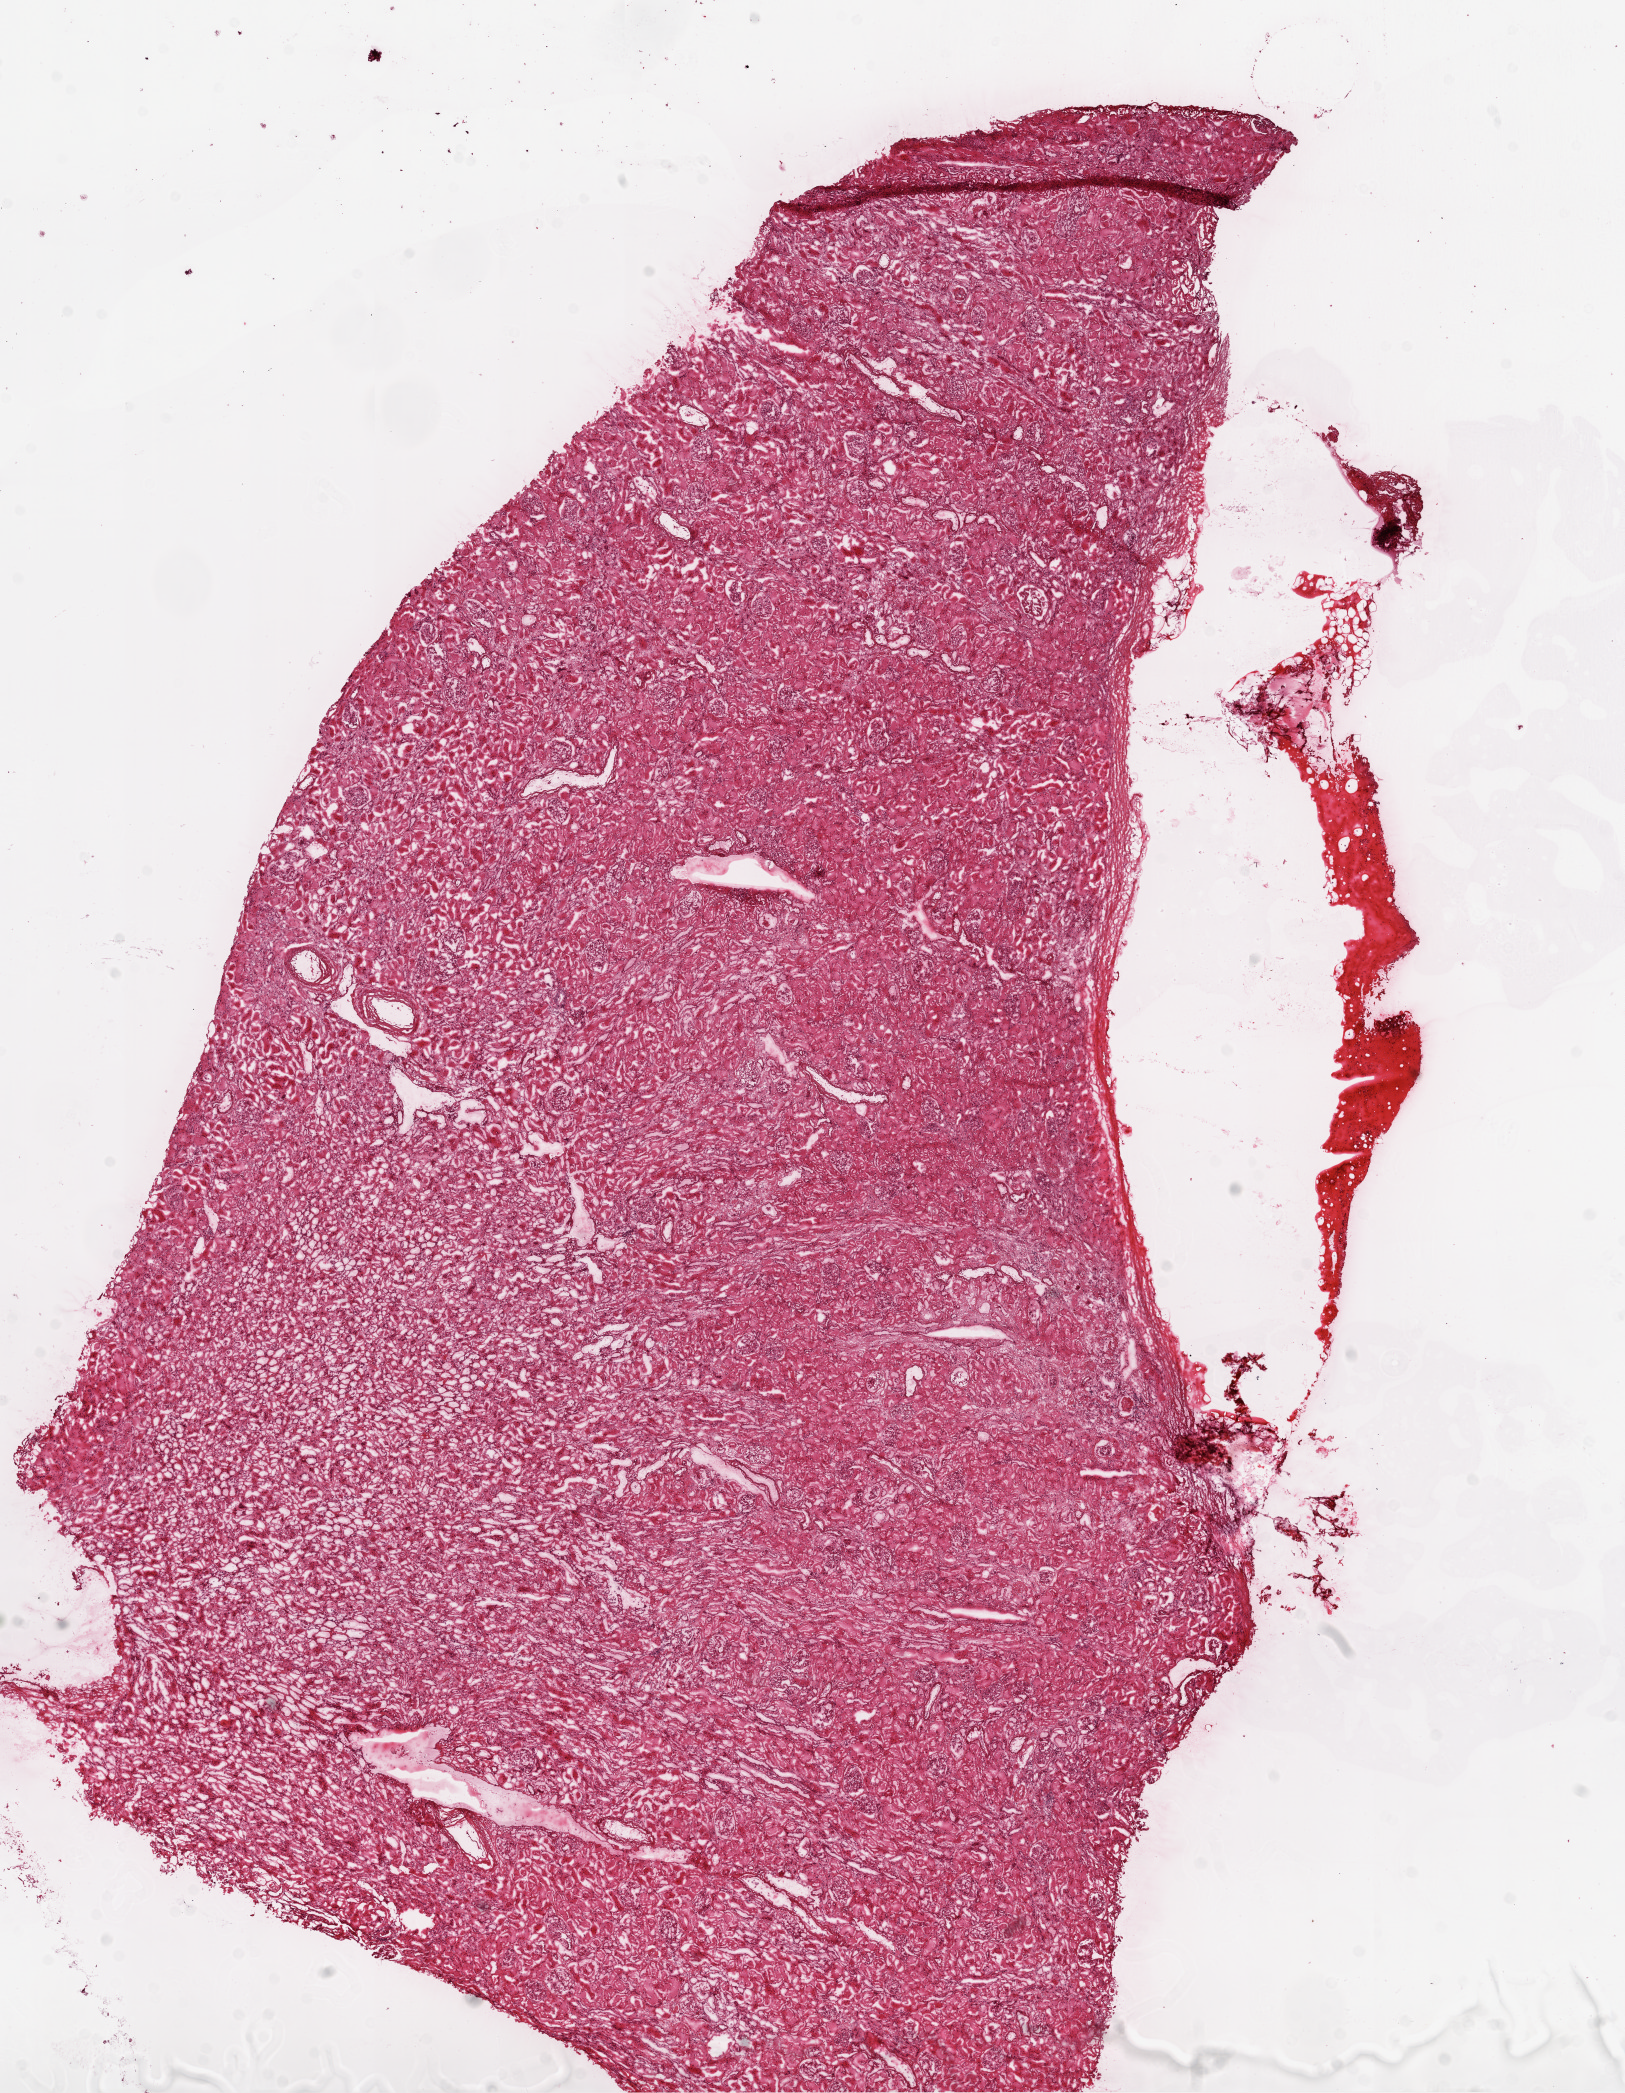
Digitized H&E-stained tissue section (whole slide), low-resolution overview of the scanned area, about 13.0 x 16.8 mm (acquisition: 20x scan). Frozen section from the top of the tissue portion. Sample: solid tissue normal (non-tumour tissue), kidney. Female patient; age at initial diagnosis 75 years.
This section: solid tissue normal (non-tumour) sample from the same patient. Patient diagnosis: Clear cell adenocarcinoma, NOS.